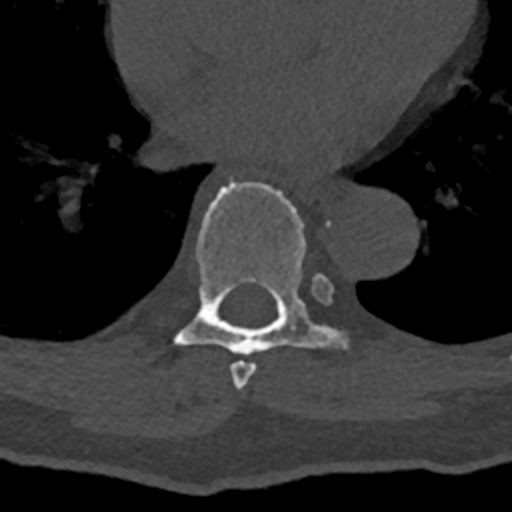
CT including the spine, one axial slice; position 715 of 797 along the scan axis; 120 kVp; bone window (W 1800 / L 400 HU); 0.5 mm slice thickness; 512 × 512 image matrix, field of view 160 × 160 mm. Male patient, age 74 years. Case-level facts recorded for this patient, not image findings: primary cancer: renal; vertebrae with lytic lesions (as recorded): T10, L1, L2, L3, L4, L5.
Annotated regions visible in this slice (semi-automatic segmentation, software-assisted and operator-edited):
- T7 vertebra: bounding box (x1, y1, x2, y2) in pixels: (230, 275, 331, 390)
- T8 vertebra: (164, 172, 348, 355)